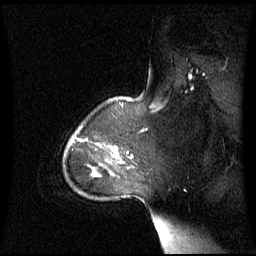
Breast MRI (dynamic contrast-enhanced), one sagittal slice; slice 51 of 60 in the series (ordered by position); dynamic contrast-enhanced series, image 2 of 3 at this slice position (ordered by acquisition); 1.5 T; TE 4.2 ms, TR 8.4 ms; 2.8 mm slice thickness; 256 × 256 image matrix, field of view 270 × 270 mm. Patient: female, 43 years. Case-level facts recorded for this patient, not image findings: setting: breast cancer imaged before/during neoadjuvant chemotherapy; receptor status: triple-negative.
Structures marked on this image (semi-automatic segmentation, software-assisted and operator-edited):
- analysis volume of interest (the breast-tissue region the enhancement analysis was run in; not a lesion): bounding box [x1, y1, x2, y2] px = [64, 125, 134, 179]
- tumour enhancement mask (voxels above the 70 % enhancement threshold inside the analysis volume of interest): [114, 152, 133, 158]